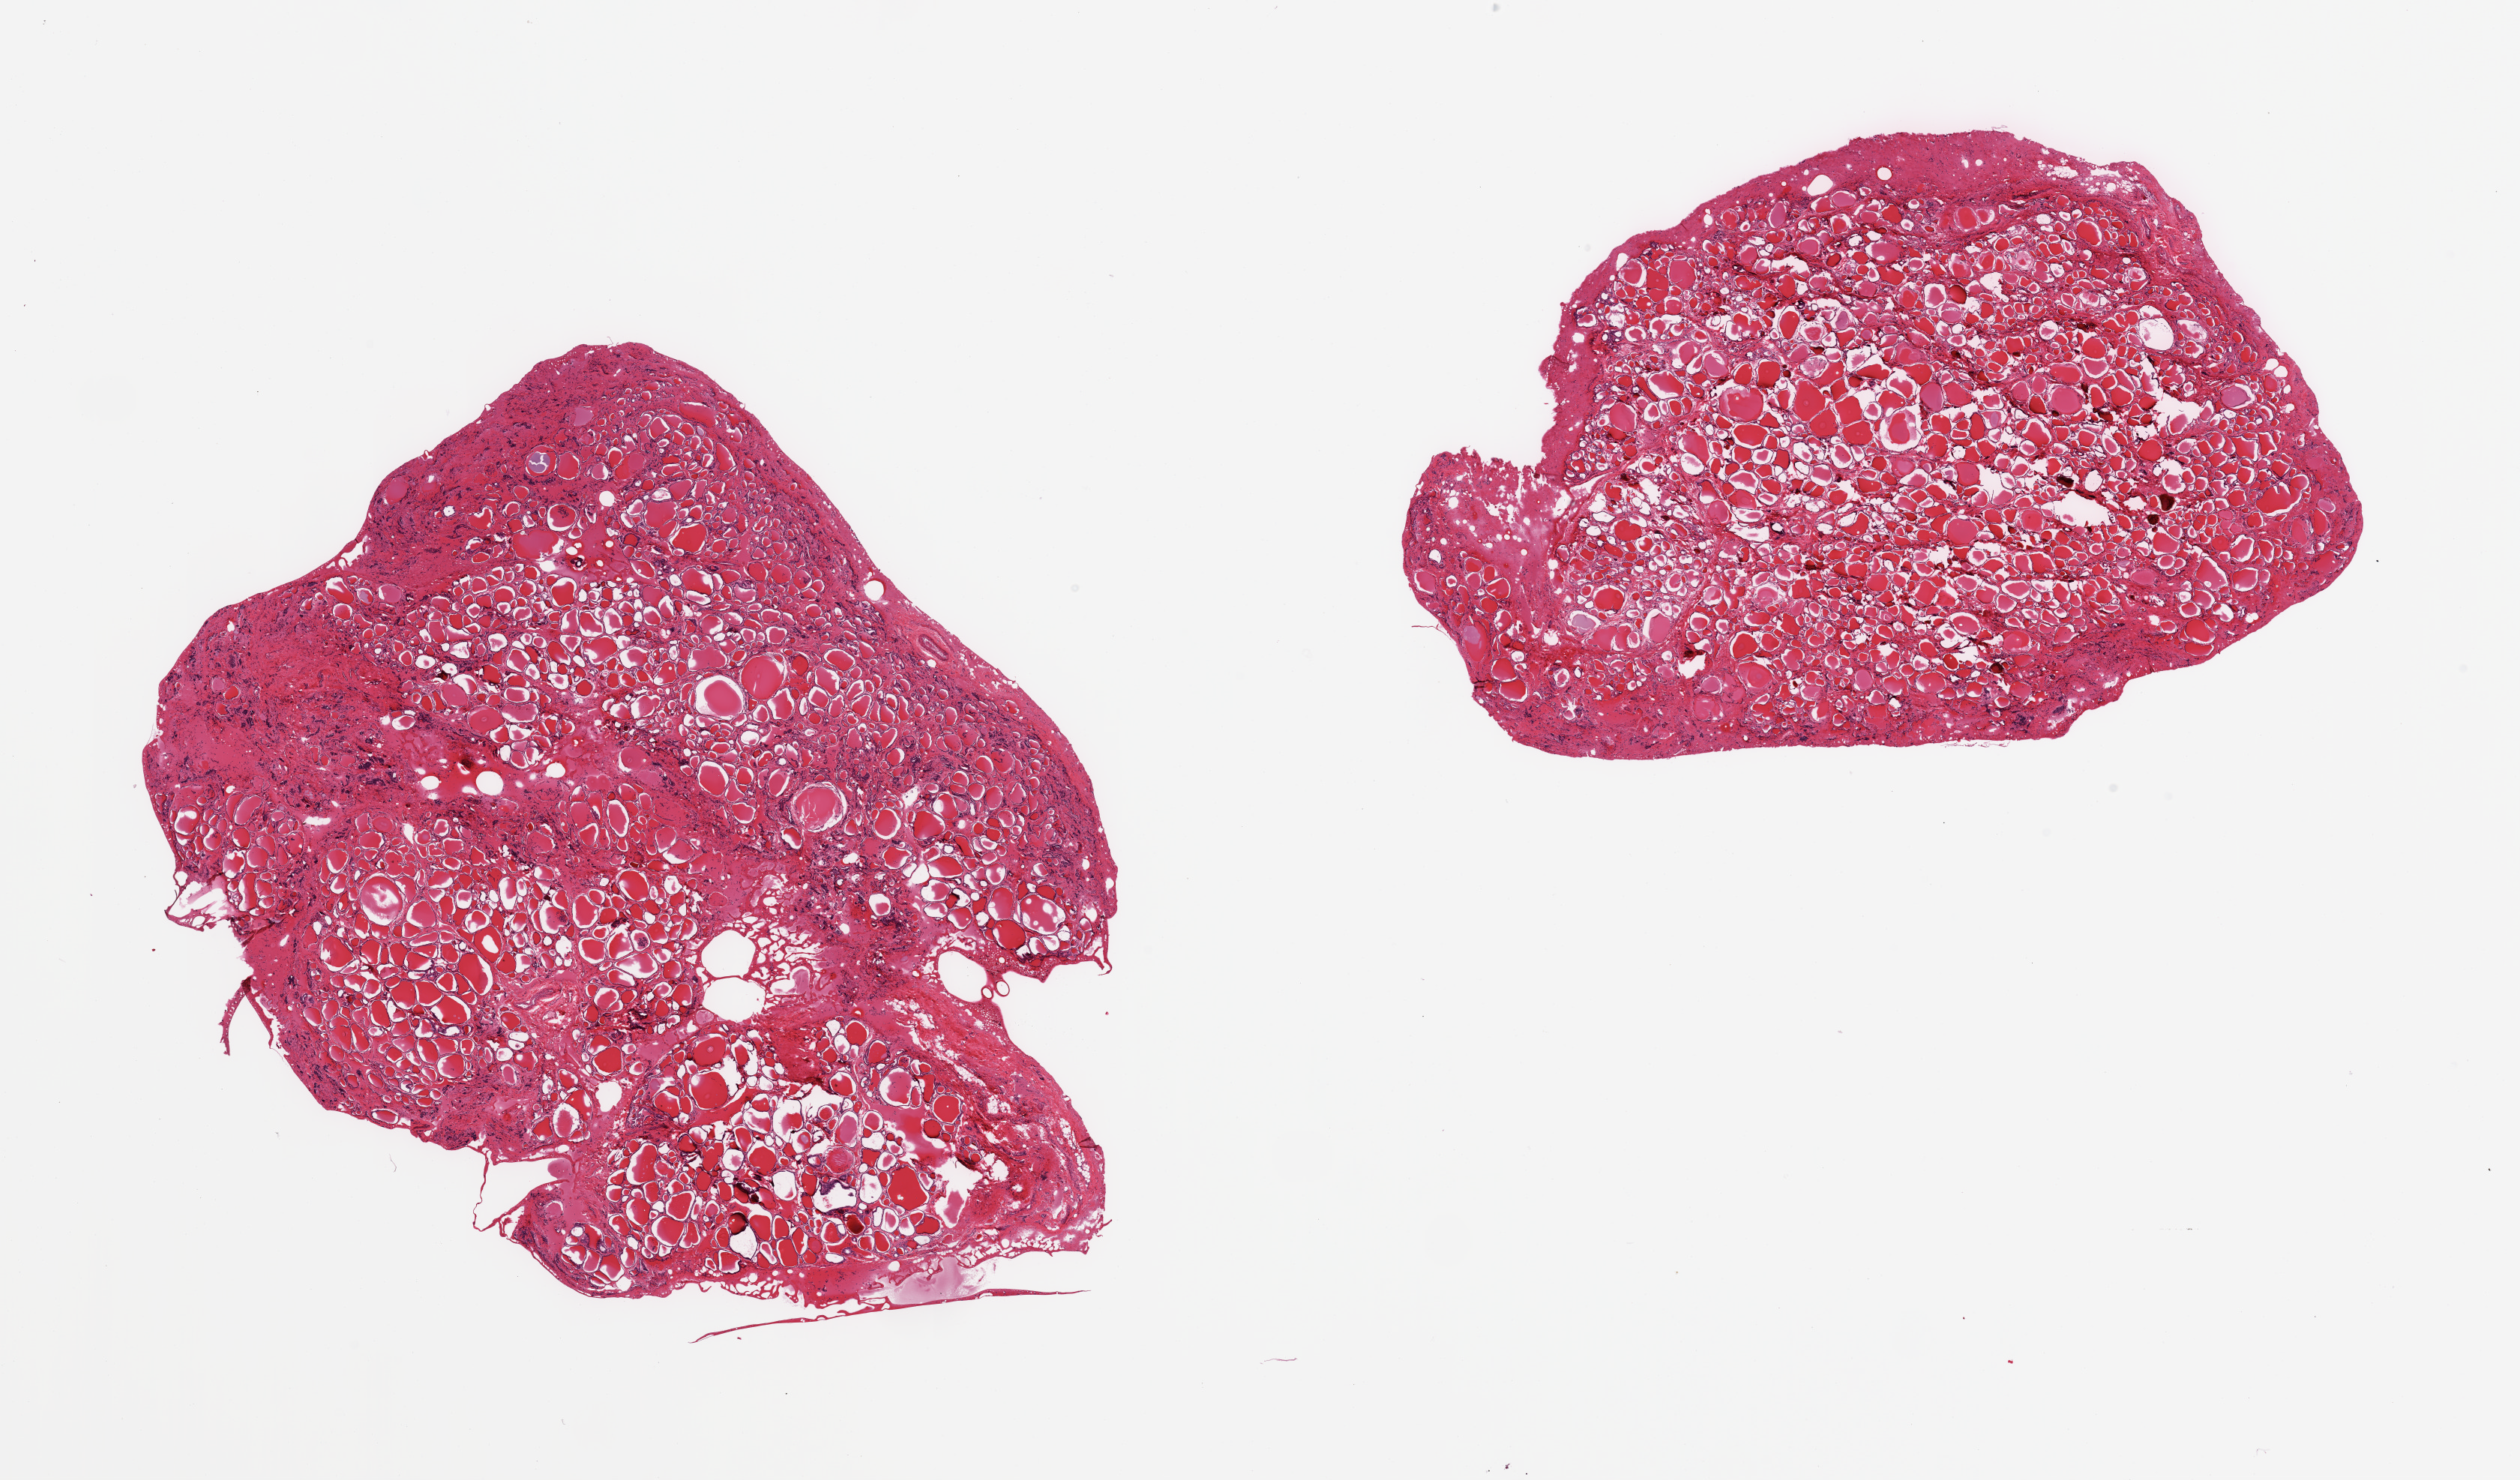
Digitized H&E-stained section — a low-resolution overview of the entire scanned area, about 26.6 x 15.6 mm (from a 20x scan), PAXgene-fixed paraffin-embedded (PFPE) section, sampled site (target tissue): thyroid, donor tissue sample.
Pathologist's review note for this sample: 2 pieces; mild to moderate autolysis; interstitial fibrosis with lobulation.